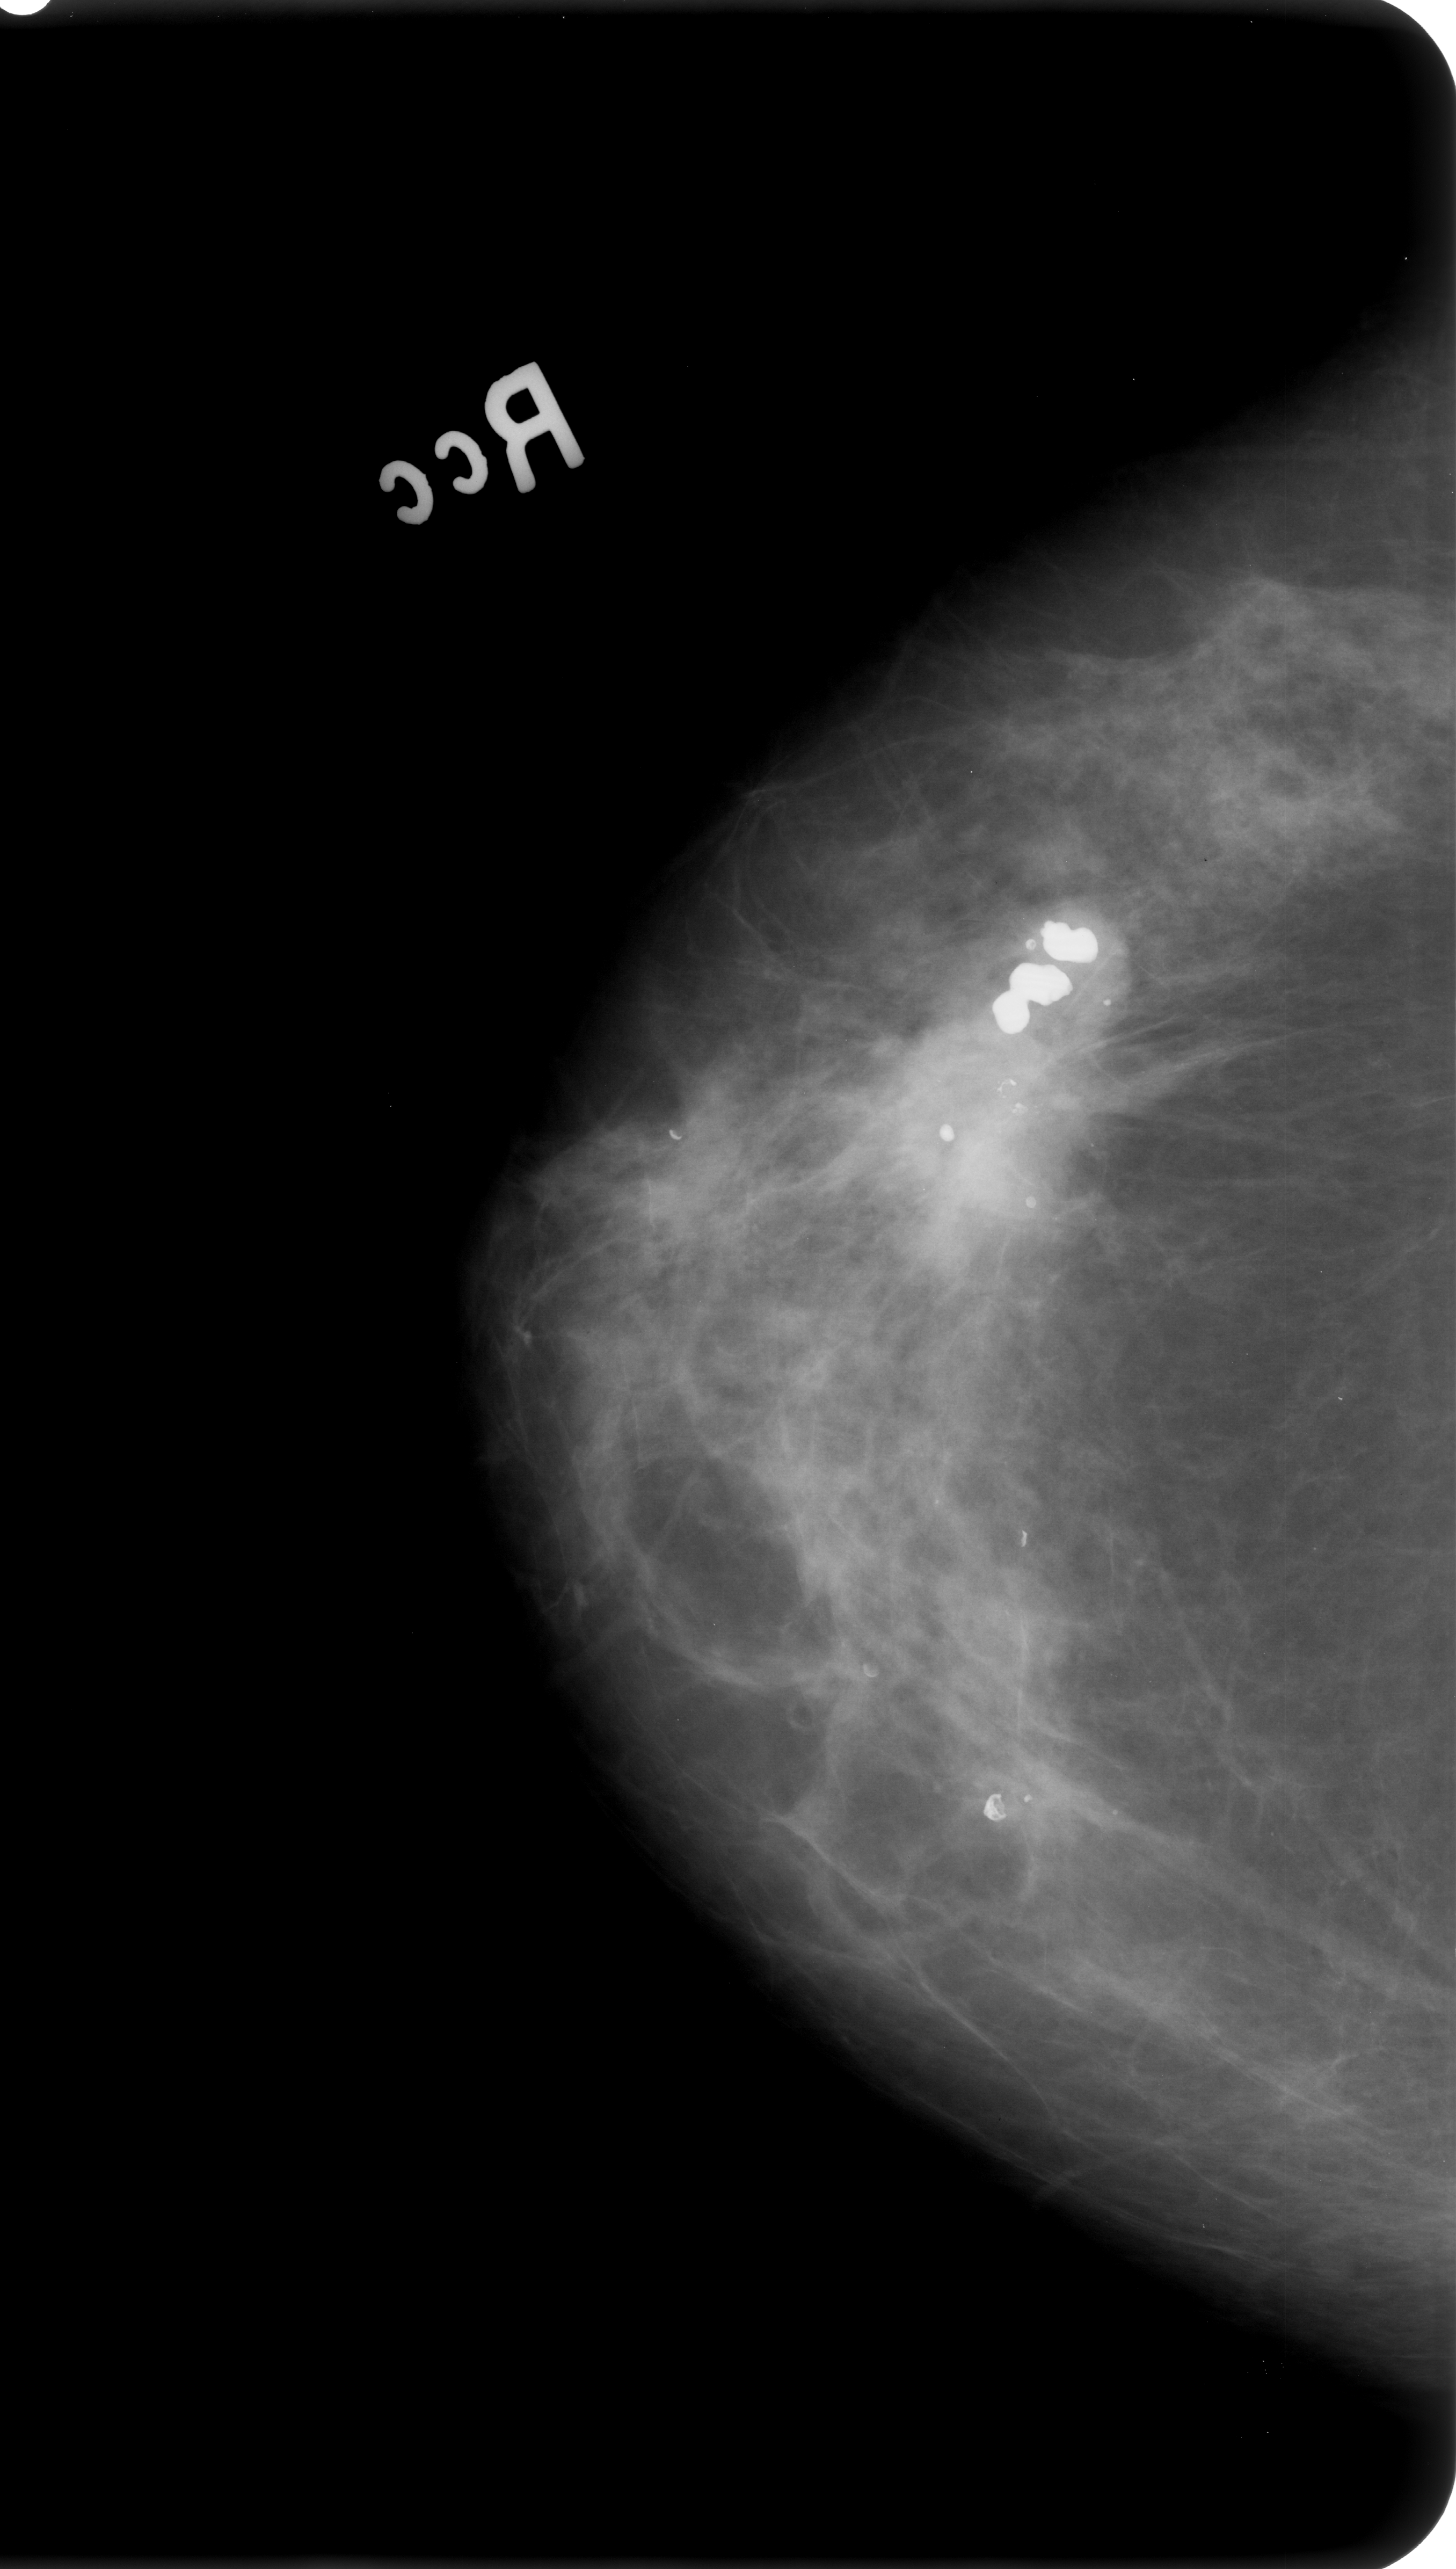
Scanned film-screen mammogram; right breast; CC view; BI-RADS breast density category 3 (scale 1–4); 1456 × 2569 image matrix.
Expert-marked regions of interest on this image (one box per marked abnormality):
- mass, shape architectural distortion, margins spiculated; BI-RADS assessment category 4; pathology (as recorded): malignant: bounding box (x1, y1, x2, y2) in pixels: (825, 922, 1157, 1204)